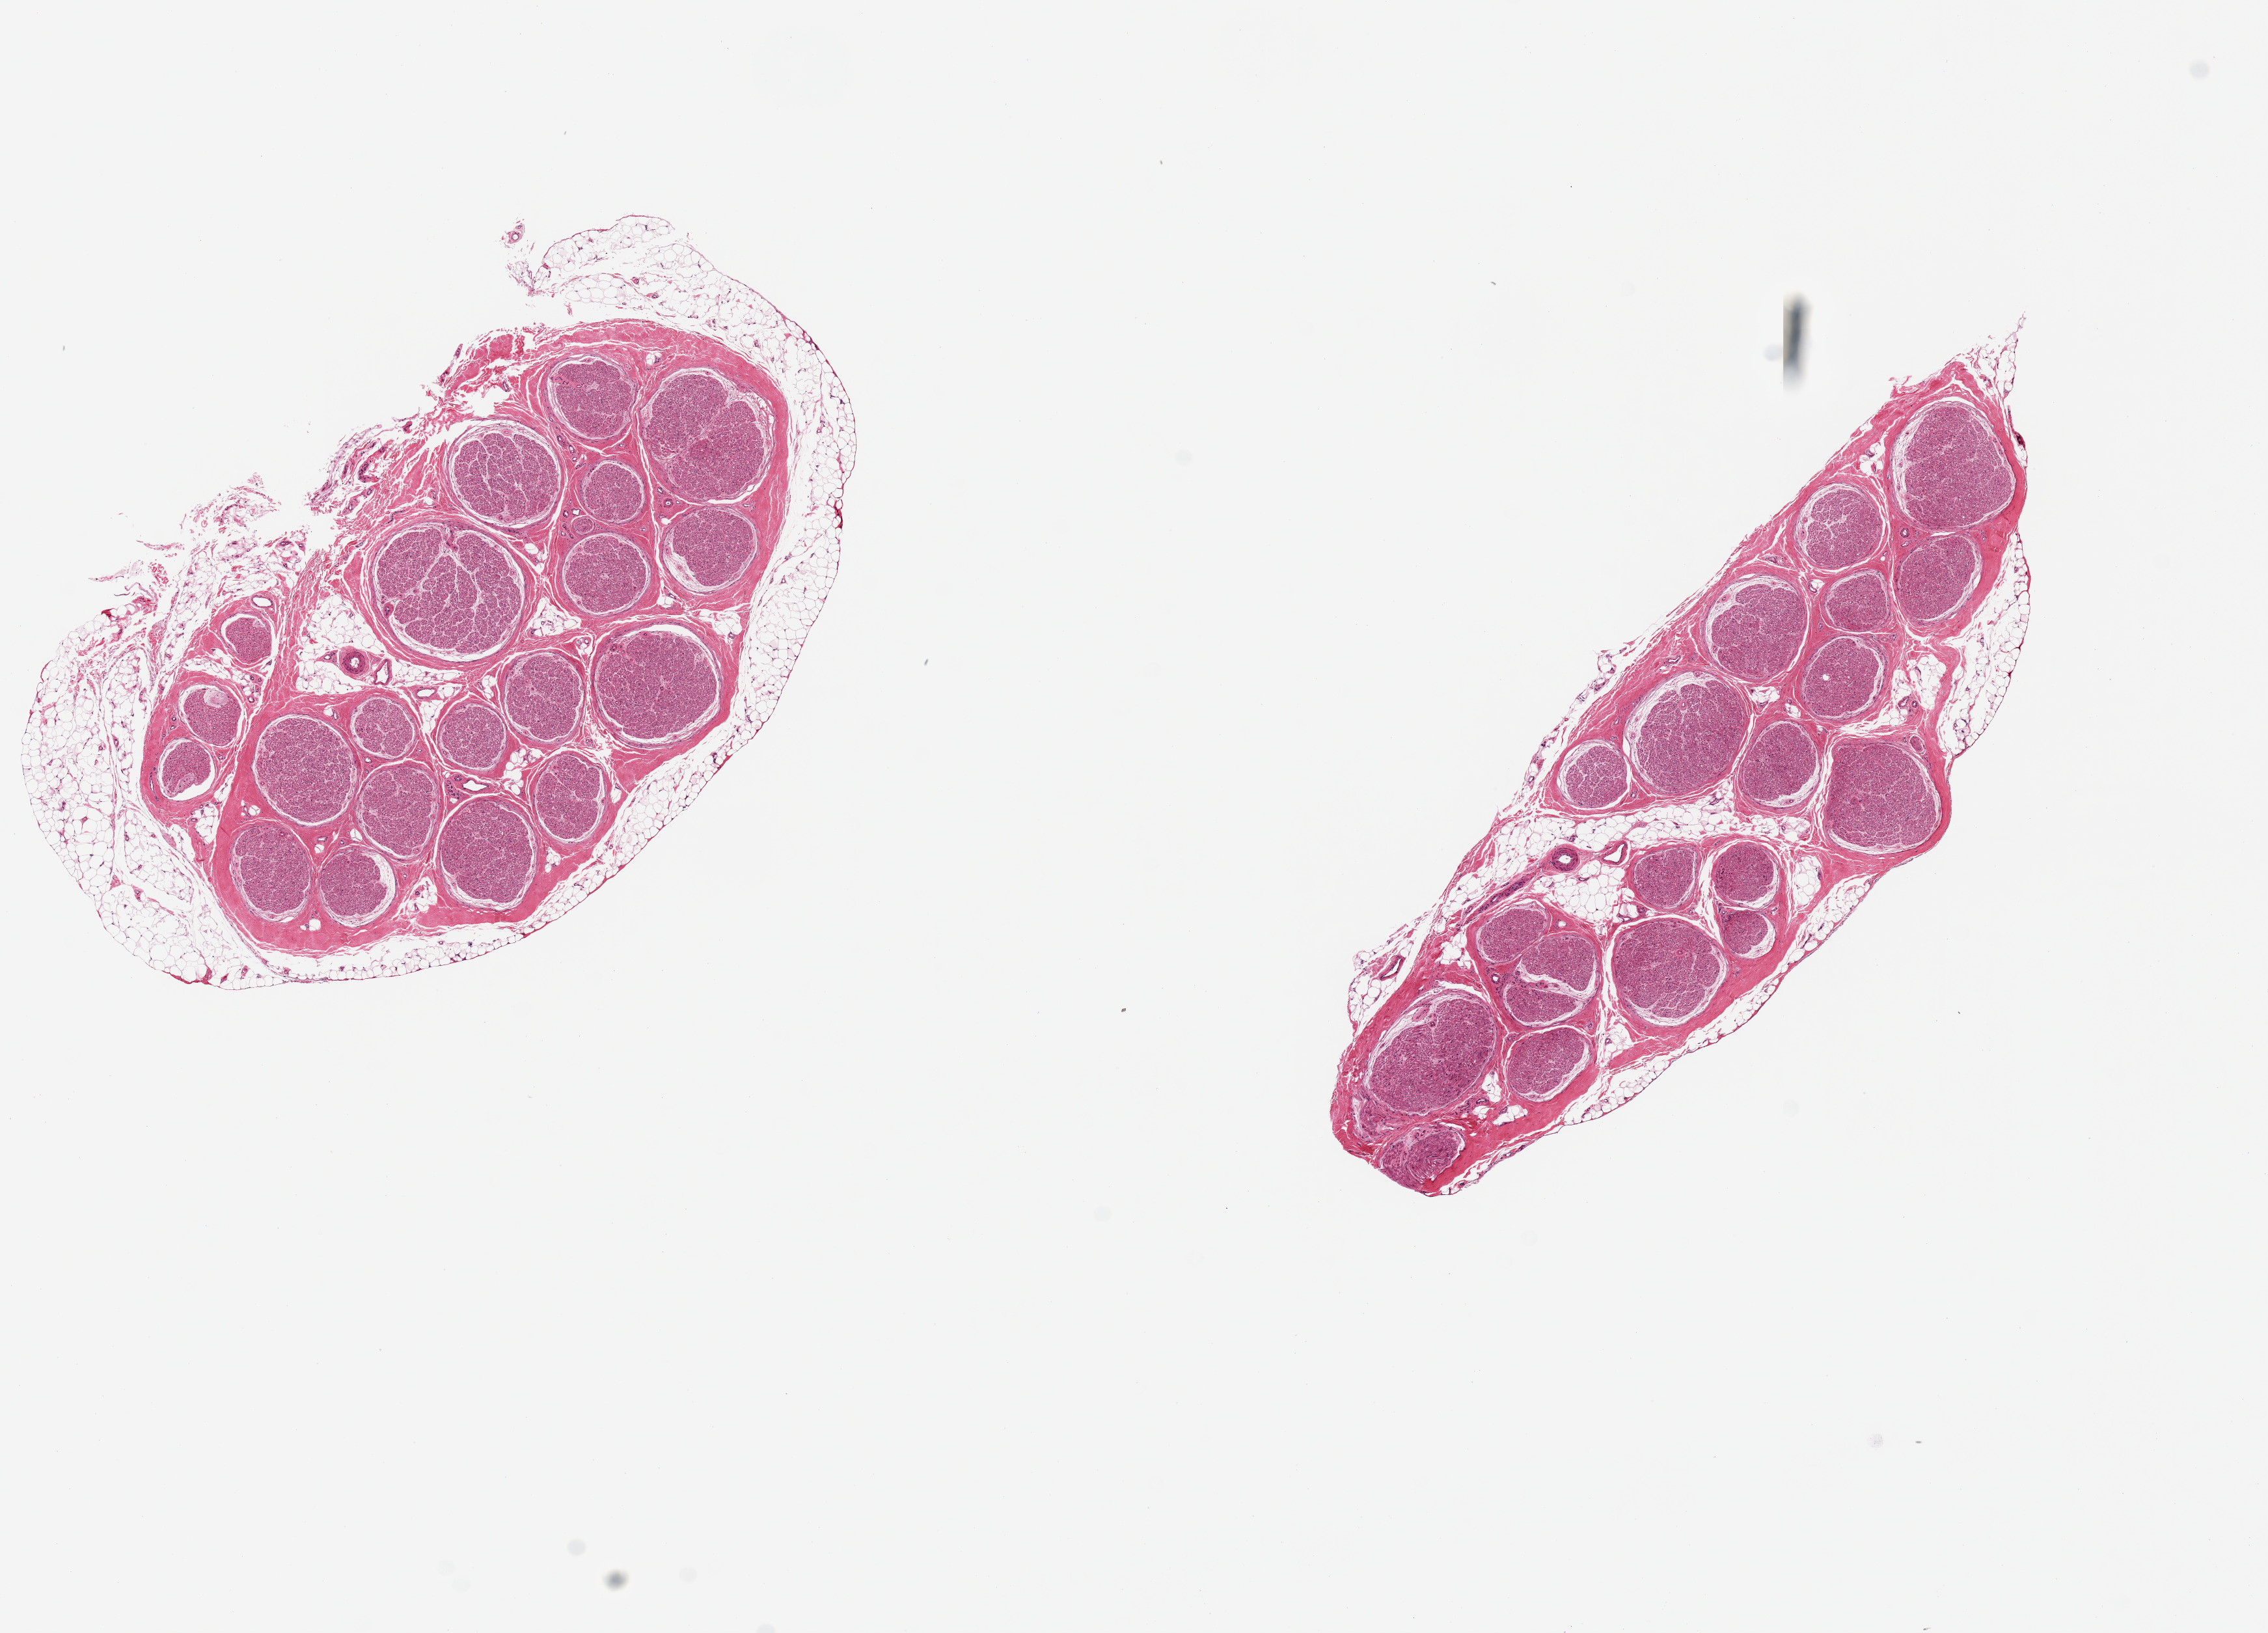
H&E whole-slide image — whole scanned area (about 13.8 x 9.9 mm, acquisition: 20x scan) shown as a low-resolution overview; PAXgene-fixed paraffin-embedded (PFPE) section; sampled site (target tissue): tibial nerve; tissue donor sample. Donor: male.
Pathologist's review note for this sample: 2 pieces, 5.5x3 & 6.5x2mm; 0.5 mm rim of adipose around 1 piece; ~10% inner and outer adipose on the other.